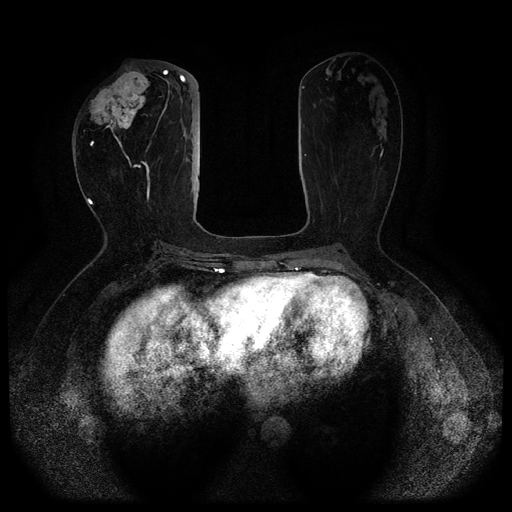
Breast MRI (dynamic contrast-enhanced, multi-phase), one axial slice; position 39 of 116 along the scan axis; dynamic contrast-enhanced series, time point 2 of 5 at this slice position (early post-contrast); 1.5 T; TE 2.6 ms, TR 5.3 ms; 2 mm slice thickness; 512 × 512 image matrix. Patient: female, 51 years.
Outlined on this slice (semi-automatically segmented with operator editing):
- breast lesion (labelled 'tumour' in the annotation; benign lesions carry a separate 'benign' label): bounding box (x1, y1, x2, y2) in pixels: (89, 69, 150, 134)